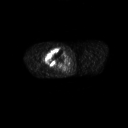
FDG PET of an extremity soft-tissue mass (from a PET/CT study), one axial slice. Slice 253 of 311 in the series (ordered by position). 3.27 mm slice thickness. 128 × 128 image matrix, field of view 700 × 700 mm. Male patient, age 50 years. From the clinical record (not read from this slice): histological type: undifferentiated - pleiomorphic; grade: high; site of the primary tumour: right thigh.
Annotated regions visible in this slice (expert contour drawn on MRI and transferred to this co-registered scan by the dataset authors):
- gross tumour volume including surrounding oedema: bounding box <42,48,65,67> (left, top, right, bottom; pixels)
- gross tumour volume (mass): <45,49,65,66>